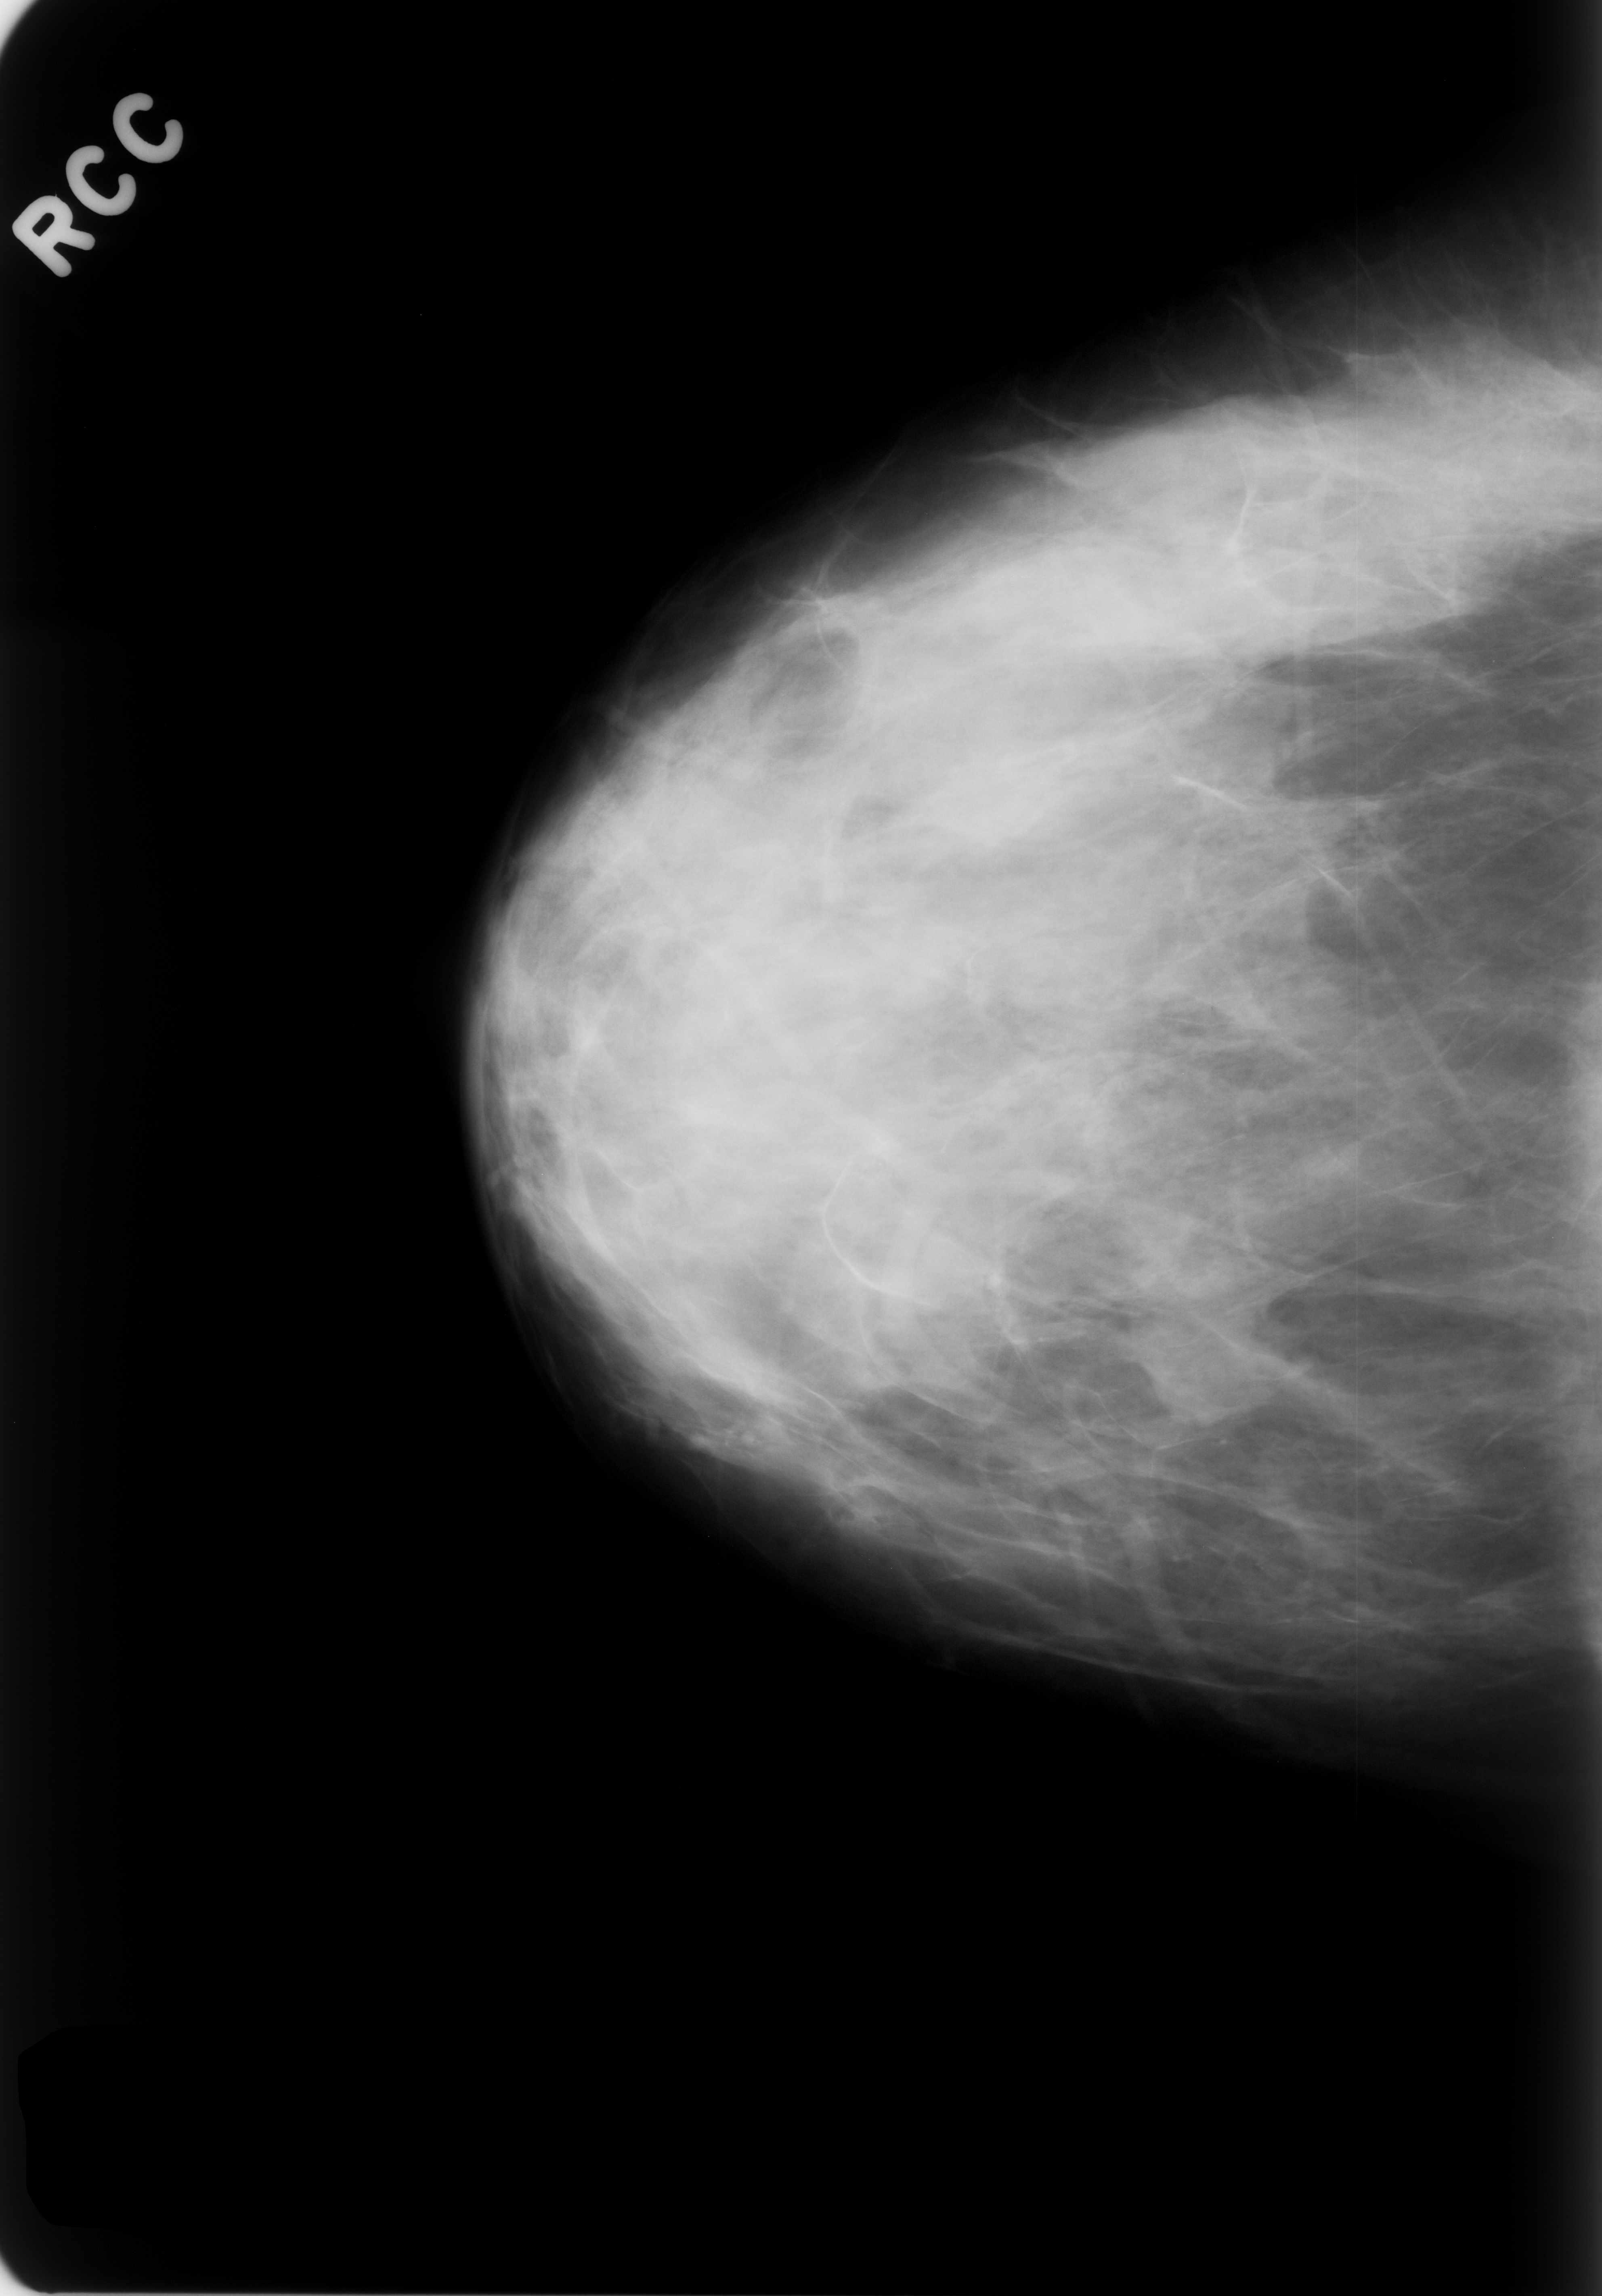
Mammogram (digitized film), right breast, craniocaudal (CC) view, BI-RADS breast density category 3 (scale 1–4).
Marked abnormality: mass, shape lobulated, margins obscured; BI-RADS assessment category 3; subtlety rating 4 on a 1 (subtle) to 5 (obvious) scale; benign; no additional work-up was recommended (benign without callback).